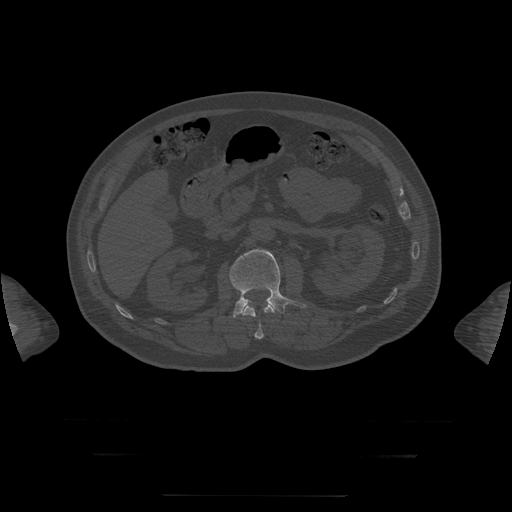
CT including the spine, one axial slice; position 32 of 397 along the scan axis; reconstruction kernel STANDARD; 120 kVp; bone window (W 1800 / L 400 HU); 1.25 mm slice thickness; 512 × 512 image matrix. Patient age 73 years. From the clinical record (not read from this slice): primary cancer: prostate.
Structures marked on this image (semi-automatically segmented with operator editing):
- L1 vertebra: bounding box (x1, y1, x2, y2) in pixels: (242, 303, 275, 340)